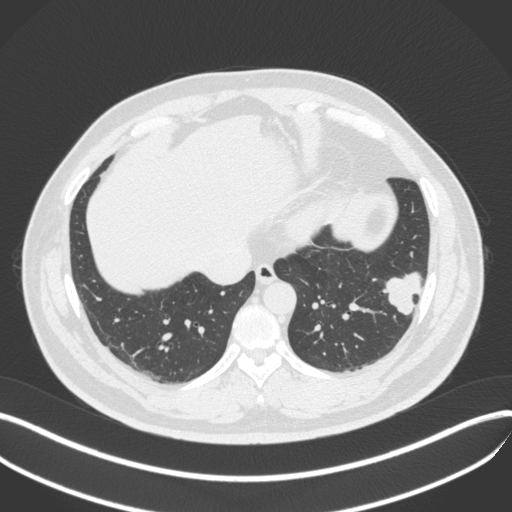
Chest CT, one axial slice. Position 124 of 420 along the scan axis. Reconstruction kernel B31f. Lung window (W 1500 / L -600 HU). 1 mm slice thickness. 512 × 512 image matrix. Male patient, age 39 years. Case-level facts recorded for this patient, not image findings: clinical TNM (as recorded): T2a N0 M0; histopathological grade: G2-3.
Annotated regions visible in this slice (bounding box drawn by a radiologist):
- lung tumour (recorded histology: adenocarcinoma): bounding box [x1, y1, x2, y2] px = [375, 268, 426, 320]